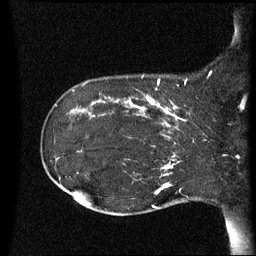
Breast MRI (dynamic contrast-enhanced), one sagittal slice. Position 19 of 60 along the scan axis. Dynamic contrast-enhanced series, image 2 of 3 at this slice position (ordered by acquisition). 1.5 T. TE 4.2 ms, TR 8.4 ms. 256 × 256 image matrix. Patient: female, 41 years. Case-level facts recorded for this patient, not image findings: setting: breast cancer imaged before/during neoadjuvant chemotherapy; receptor status: HER2-positive.
Outlined on this slice (semi-automatic segmentation, software-assisted and operator-edited):
- analysis volume of interest (the breast-tissue region the enhancement analysis was run in; not a lesion): box from (x=122, y=84) to (x=195, y=137) px
- tumour enhancement mask (voxels above the 70 % enhancement threshold inside the analysis volume of interest): (x=125, y=84)–(x=186, y=137)